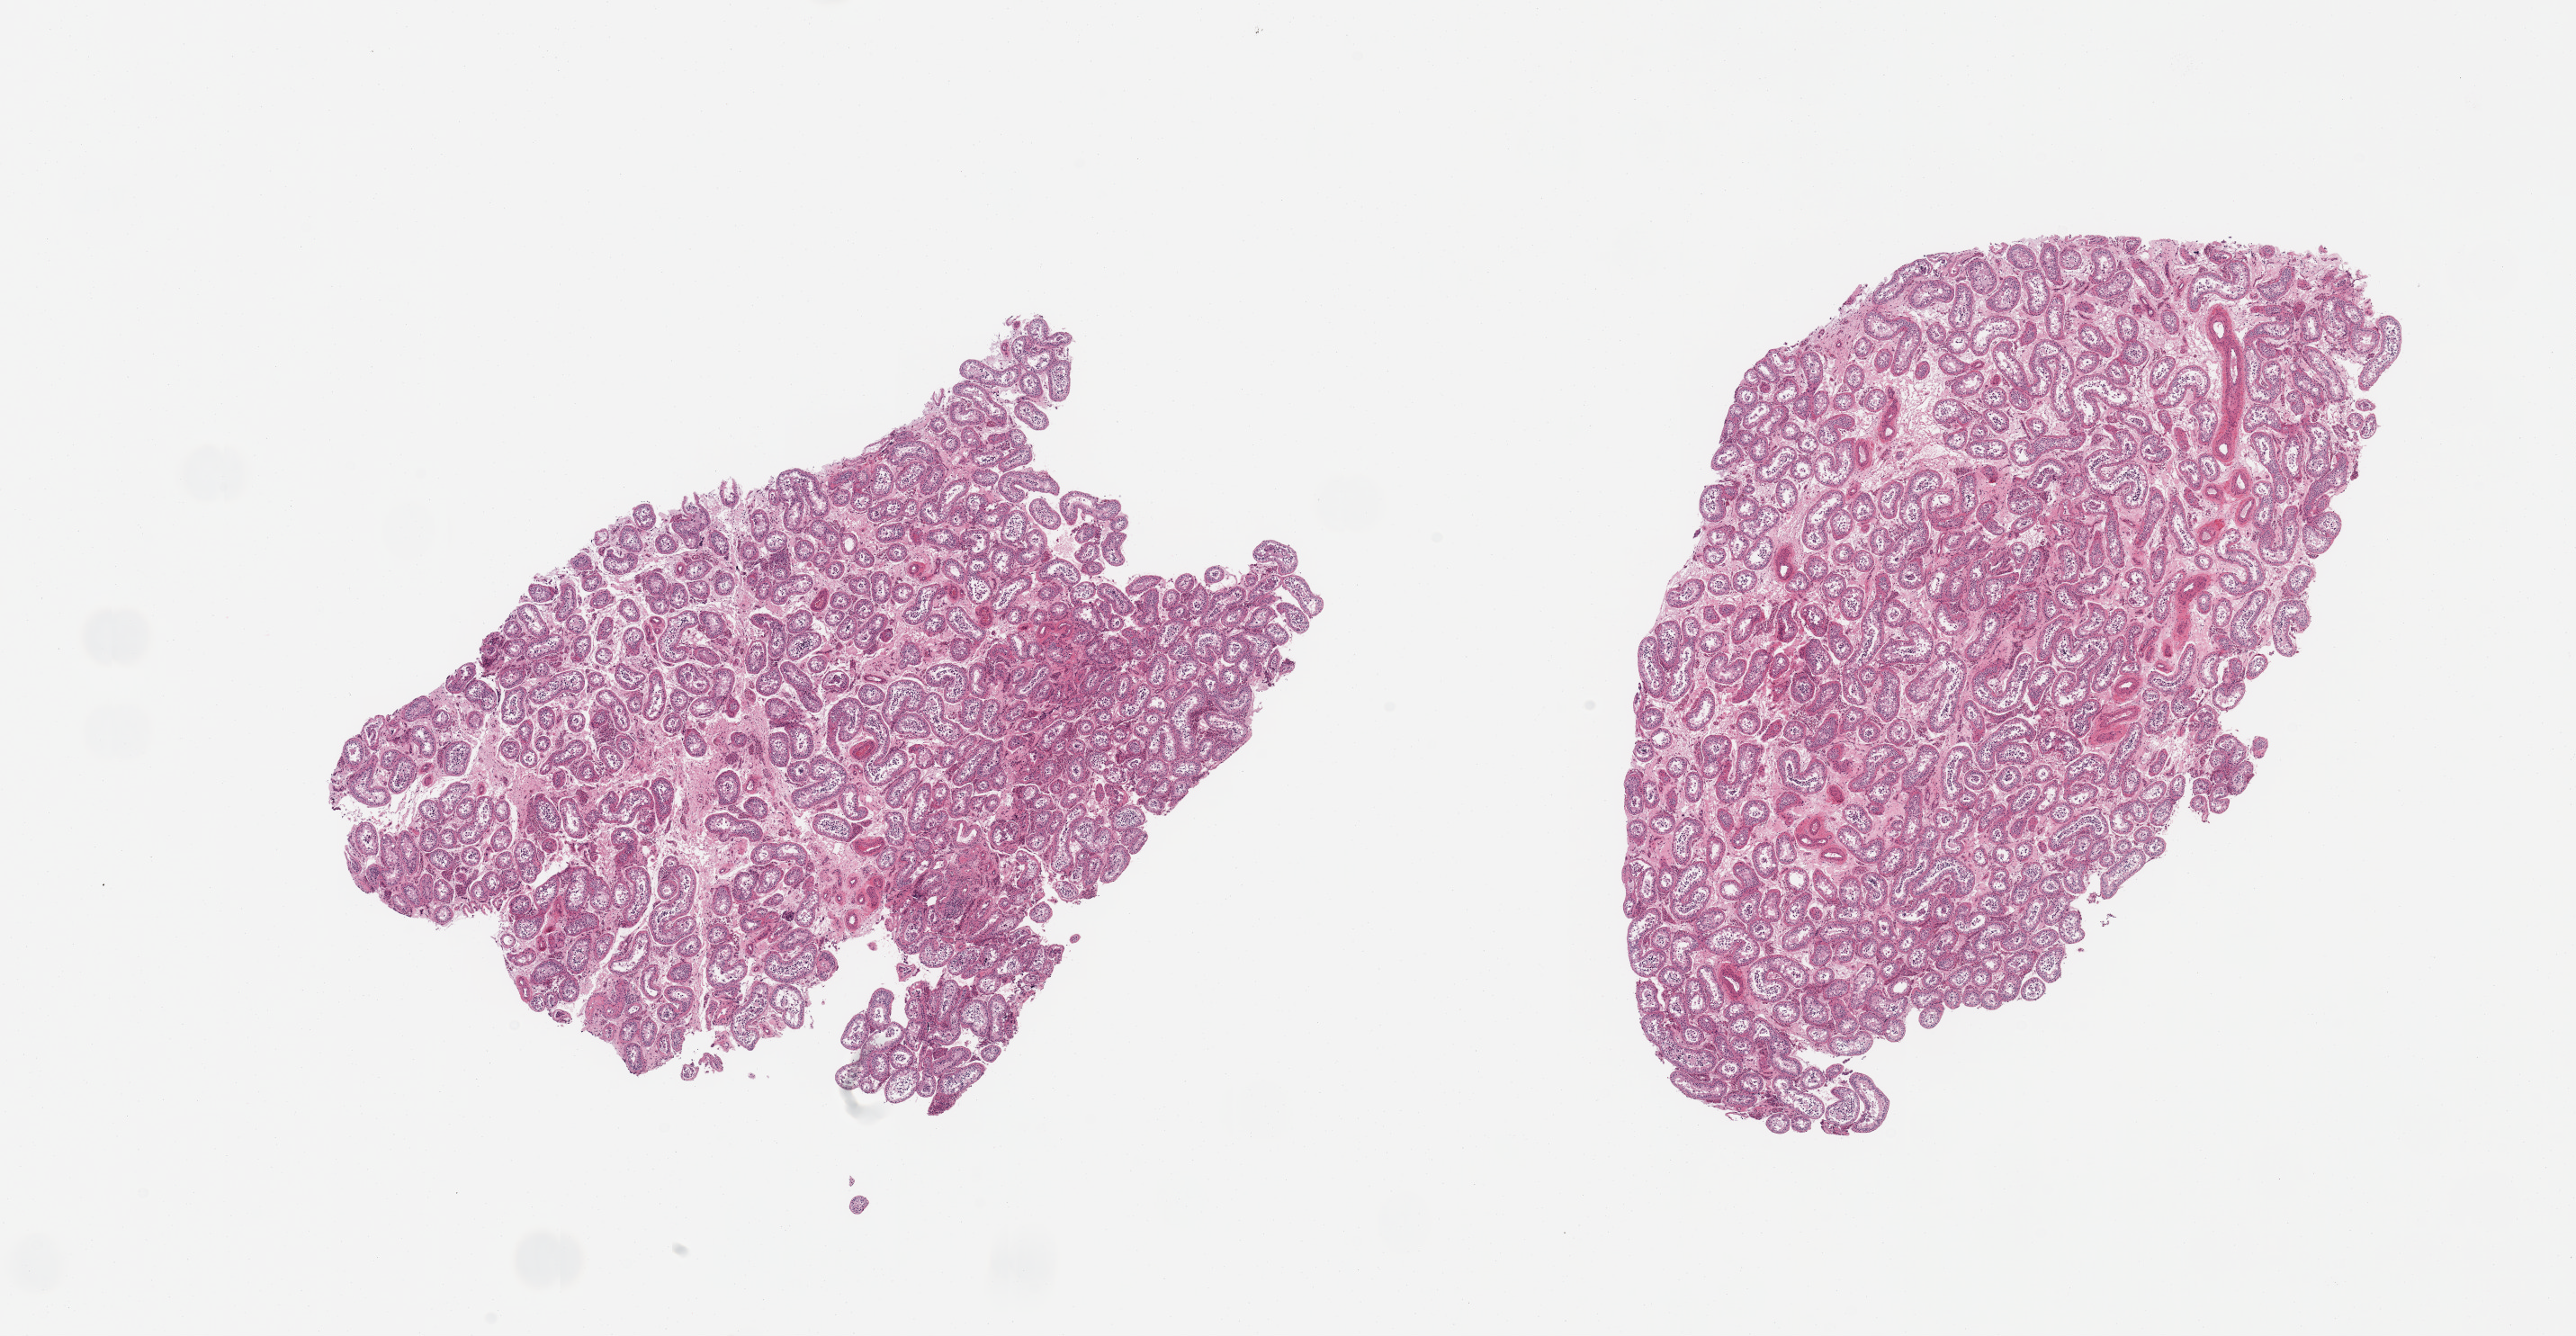
Hematoxylin and eosin (H&E) whole-slide image — shown as a low-resolution overview of the whole scanned area (about 22.6 x 11.7 mm, acquisition: 20x scan); PAXgene-fixed paraffin-embedded (PFPE) section; target tissue: testis; donor tissue sample.
Pathologist's review note for this sample: 2 pieces; moderate decrease in mature spermatogenesis.